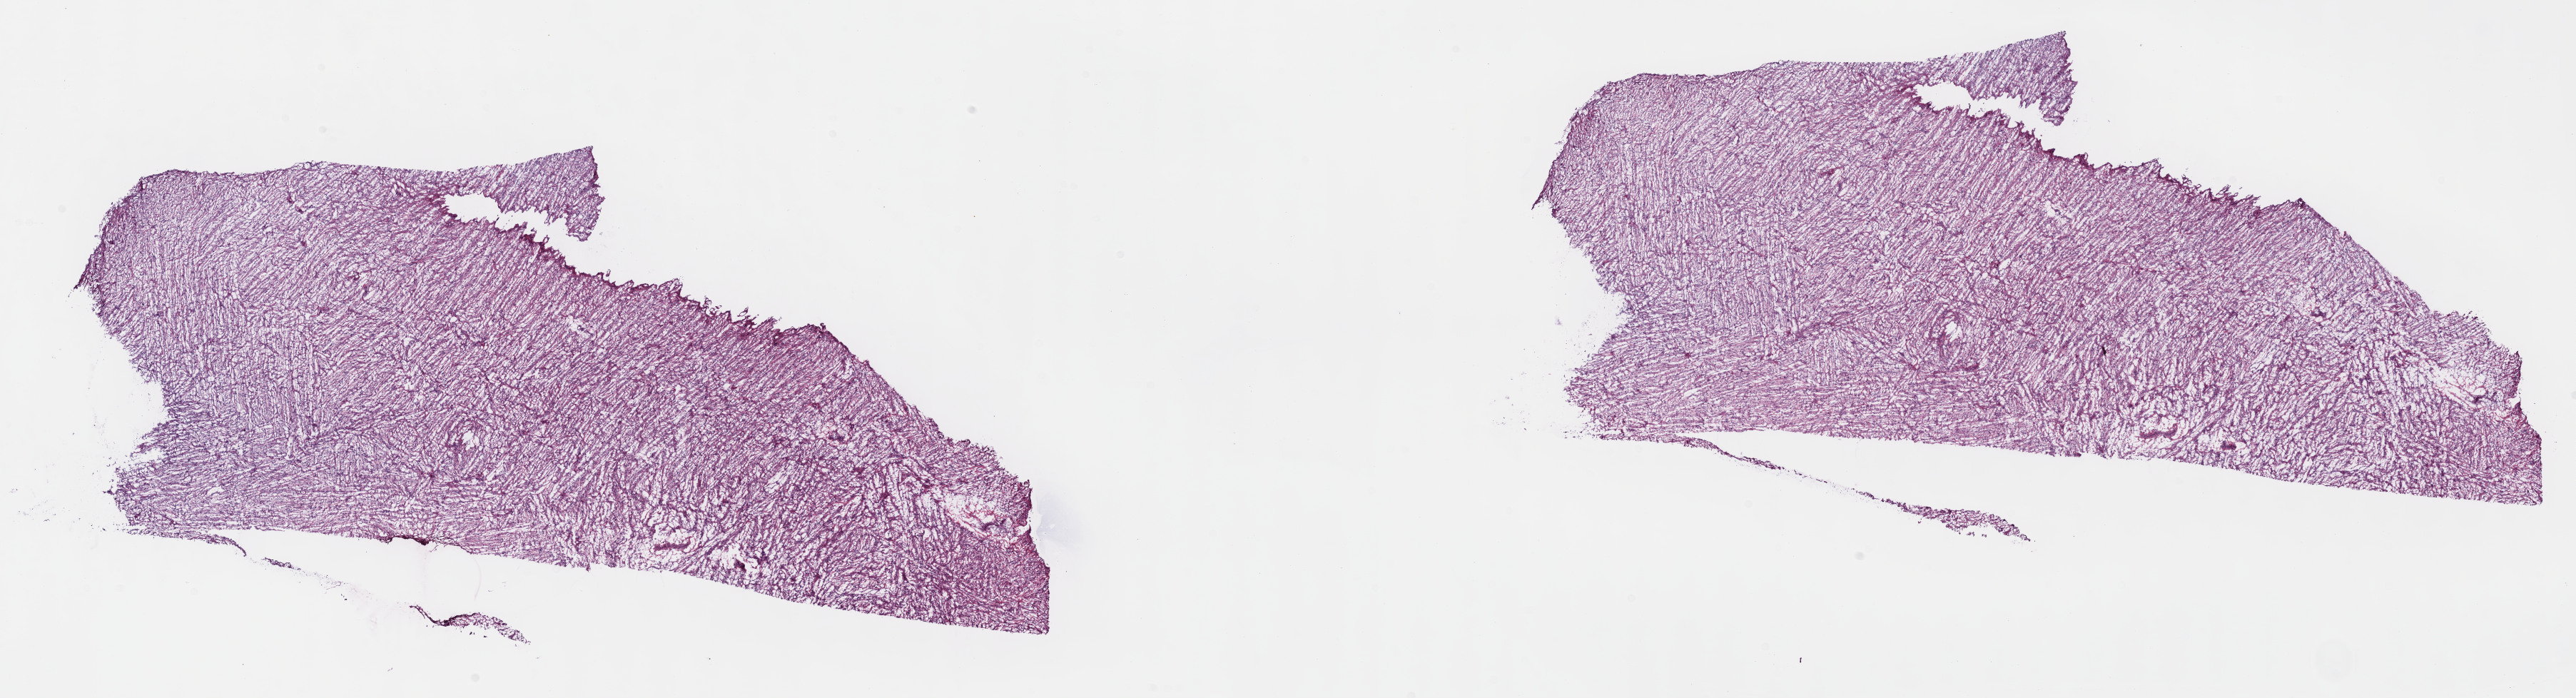
Digitized H&E-stained tissue section (whole slide), whole scanned area (about 29.2 x 7.9 mm) shown as a low-resolution overview. Frozen section from the top of the tissue portion. Retroperitoneum and peritoneum, primary tumour sample. Female patient; age at initial diagnosis 76 years. Composition of this section per pathologist review: tumour cells 75%, tumour nuclei 75%, normal cells 0%, stromal cells 25%, necrosis 0%. Inflammatory infiltration, as recorded: lymphocyte infiltration 2%, monocyte infiltration 1%, neutrophil infiltration 3%.
Pathologic diagnosis: Dedifferentiated liposarcoma (retroperitoneum).